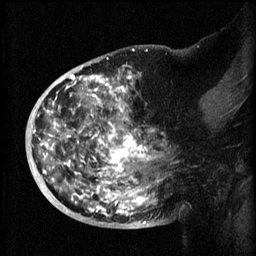
Breast MRI (dynamic contrast-enhanced), one sagittal slice; position 30 of 60 along the scan axis; 3 images stored at this slice position (order not interpretable as contrast timing); 1.5 T; TE 4.2 ms, TR 8.2 ms; 2 mm slice thickness; 256 × 256 image matrix. Patient: female, 50 years.
Outlined on this slice (semi-automatically segmented with operator editing):
- analysis volume of interest (the breast-tissue region the enhancement analysis was run in; not a lesion): bounding box <44,72,171,219> (left, top, right, bottom; pixels)
- tumour enhancement mask (voxels above the 70 % enhancement threshold inside the analysis volume of interest): <44,72,162,217>